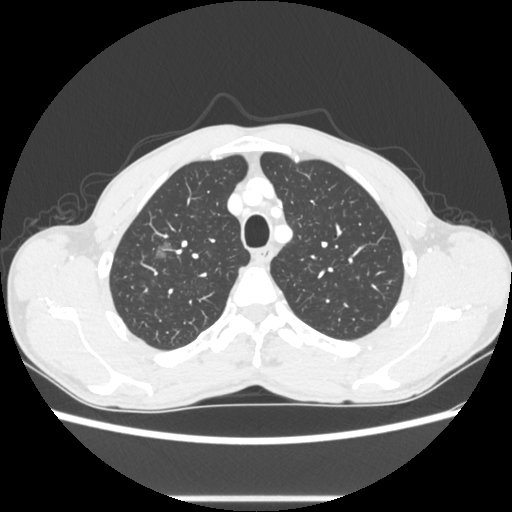
Chest CT, one axial slice; slice 227 of 289 in the series (ordered by position); 100 kVp; lung window (W 1500 / L -600 HU); 1.25 mm slice thickness; 512 × 512 image matrix. Male patient, age 54 years. Case-level facts recorded for this patient, not image findings: clinical TNM (as recorded): T1a N0 M0.
Annotated regions visible in this slice (rectangle marked by the reading radiologist):
- lung tumour (recorded histology: adenocarcinoma): bounding box <151,229,178,270> (left, top, right, bottom; pixels)